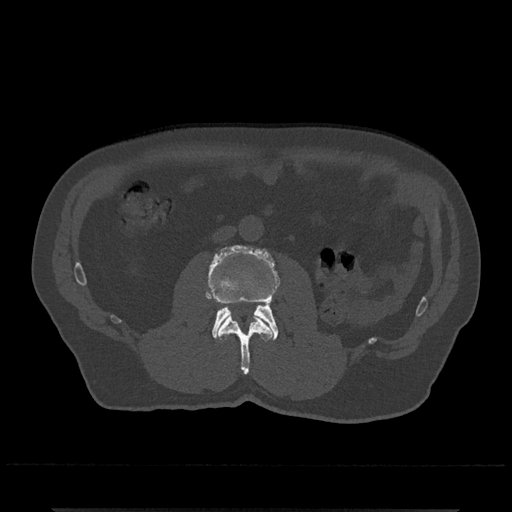
CT including the spine, one axial slice. Reconstruction kernel Br40s/3. Bone window (W 1800 / L 400 HU). 0.5 mm slice thickness. 512 × 512 image matrix. Patient: male, 67 years. Case-level facts recorded for this patient, not image findings: primary cancer: prostate.
Annotated regions visible in this slice (semi-automatic segmentation, software-assisted and operator-edited):
- L2 vertebra: bounding box (x1, y1, x2, y2) in pixels: (217, 314, 273, 374)
- L3 vertebra: (206, 245, 279, 341)